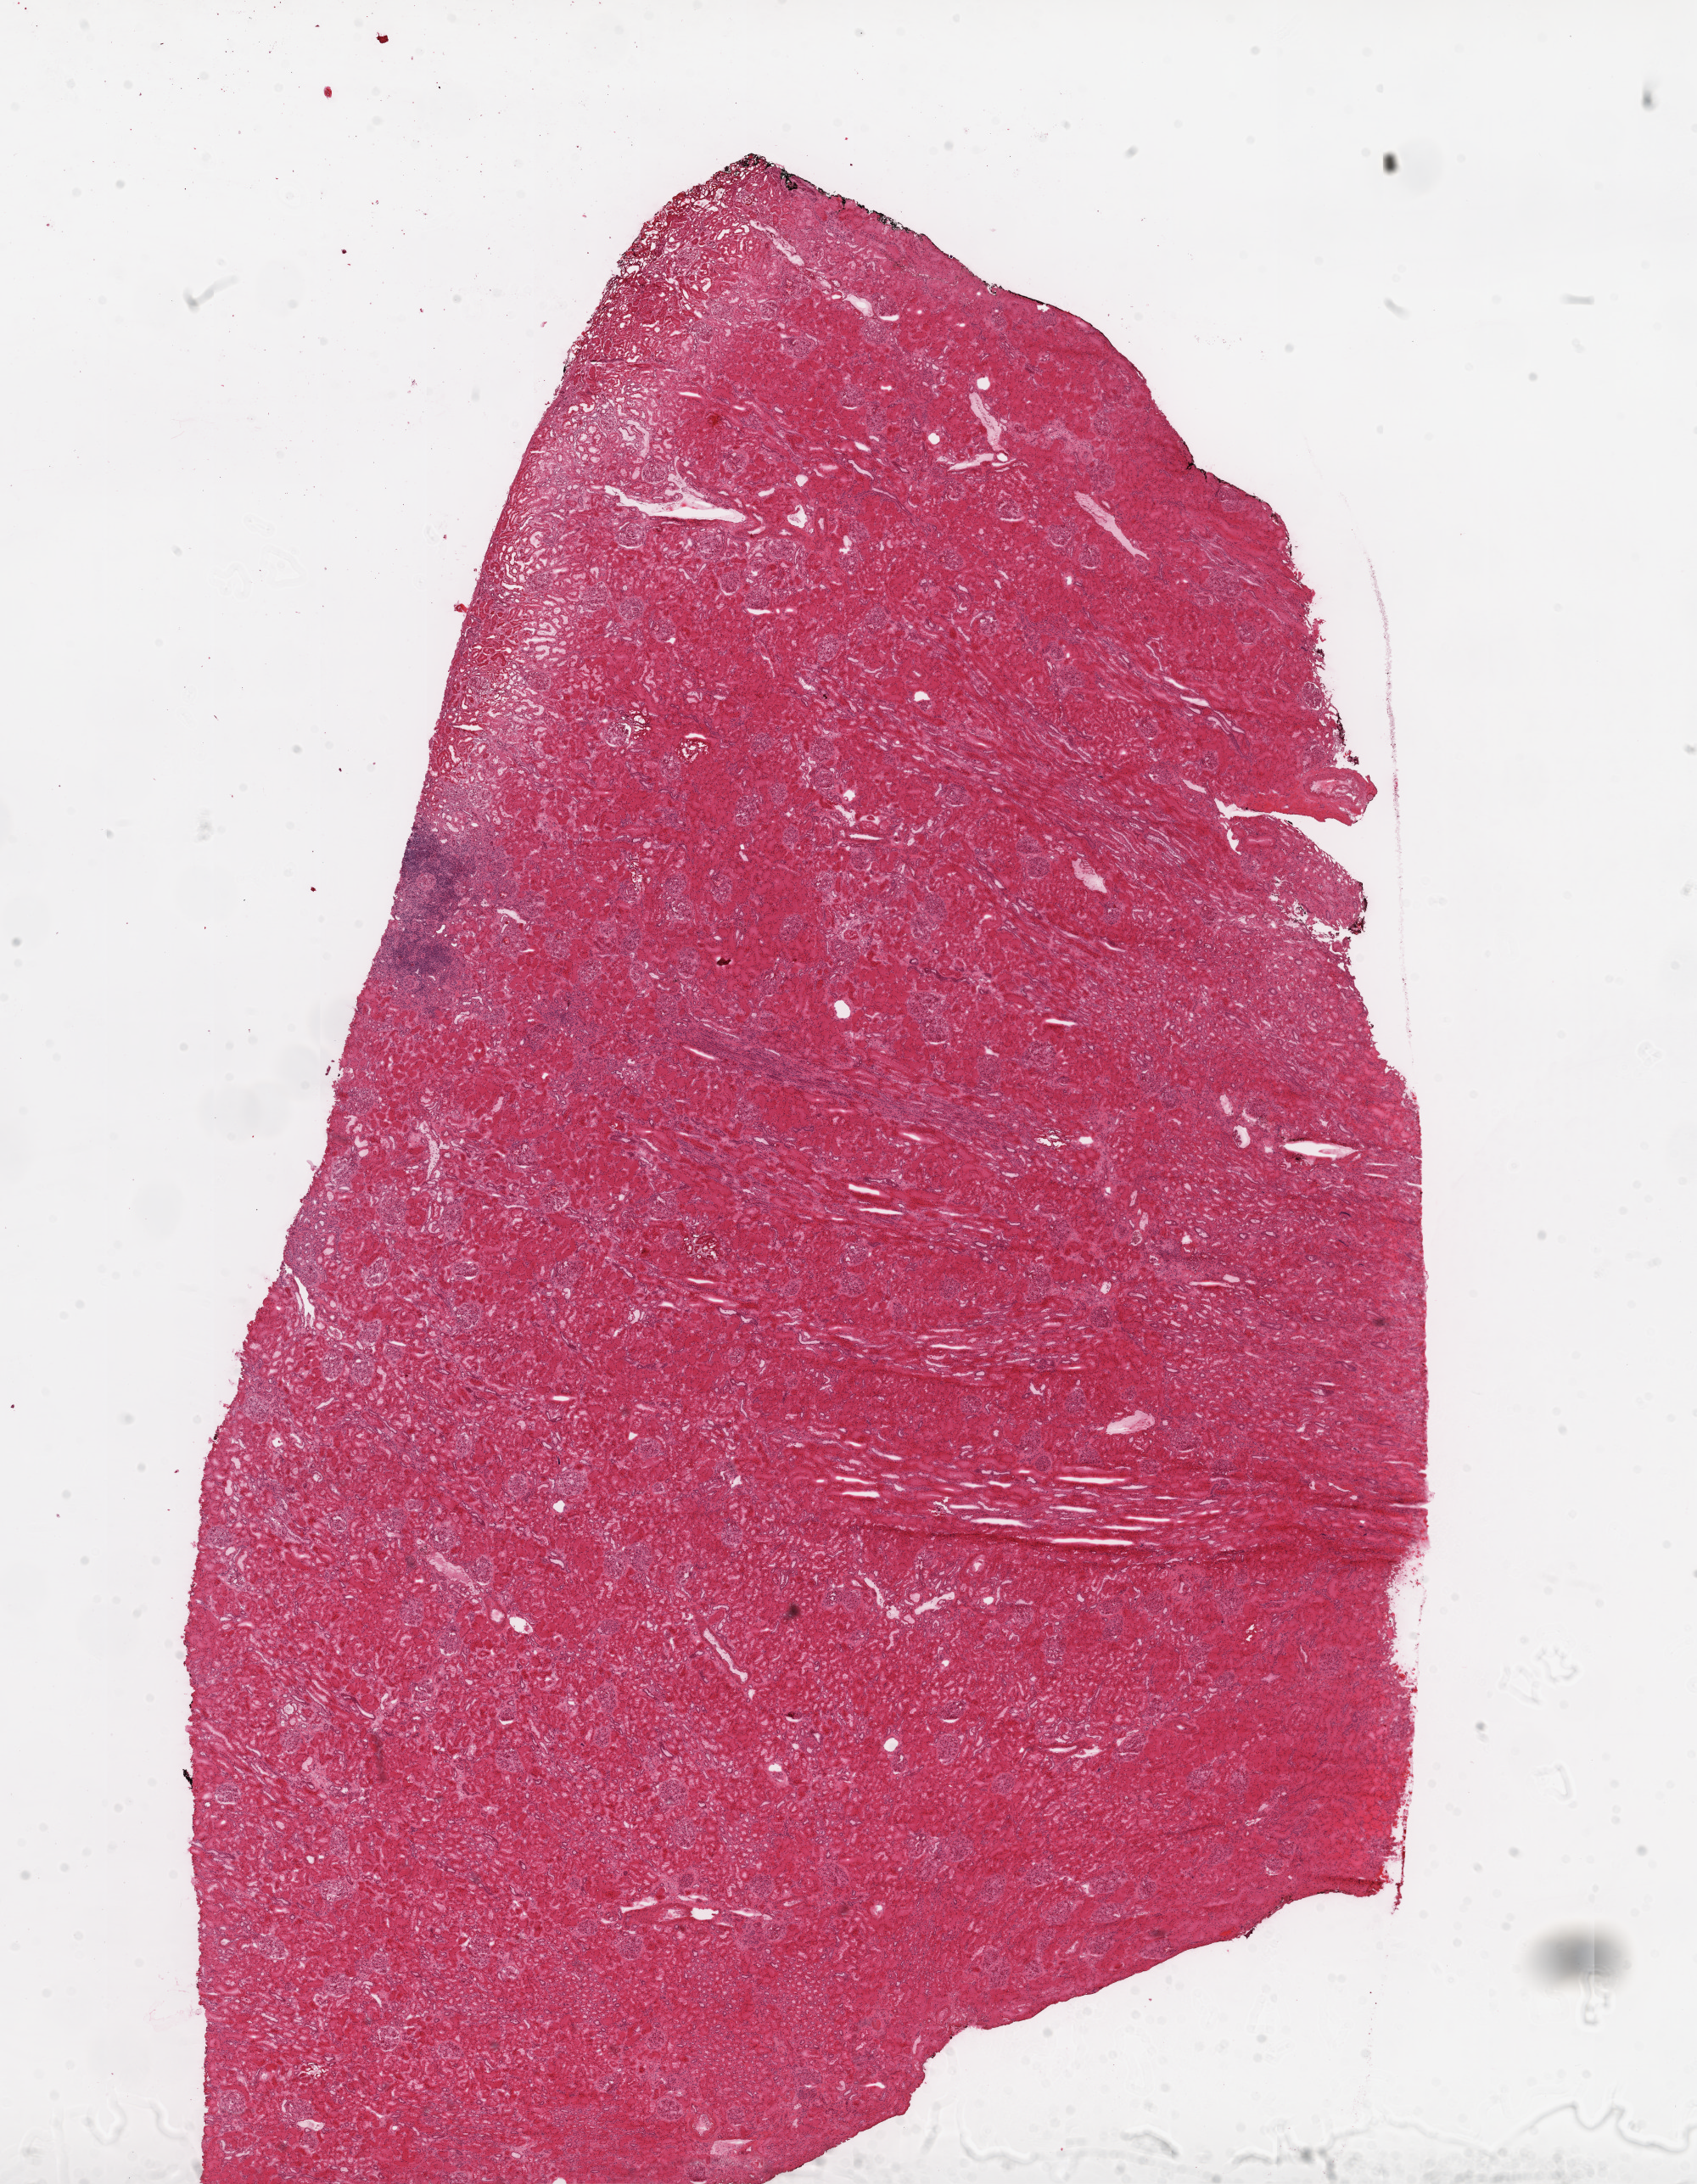
Whole-slide histology image, H&E — low-resolution overview of the scanned area, about 16.0 x 20.7 mm, frozen section, solid tissue normal (non-tumour tissue) sample from the kidney. Patient: male, age at initial diagnosis 42 years.
This section: solid tissue normal sample (biorepository sample class). Patient diagnosis: Clear cell adenocarcinoma, NOS.